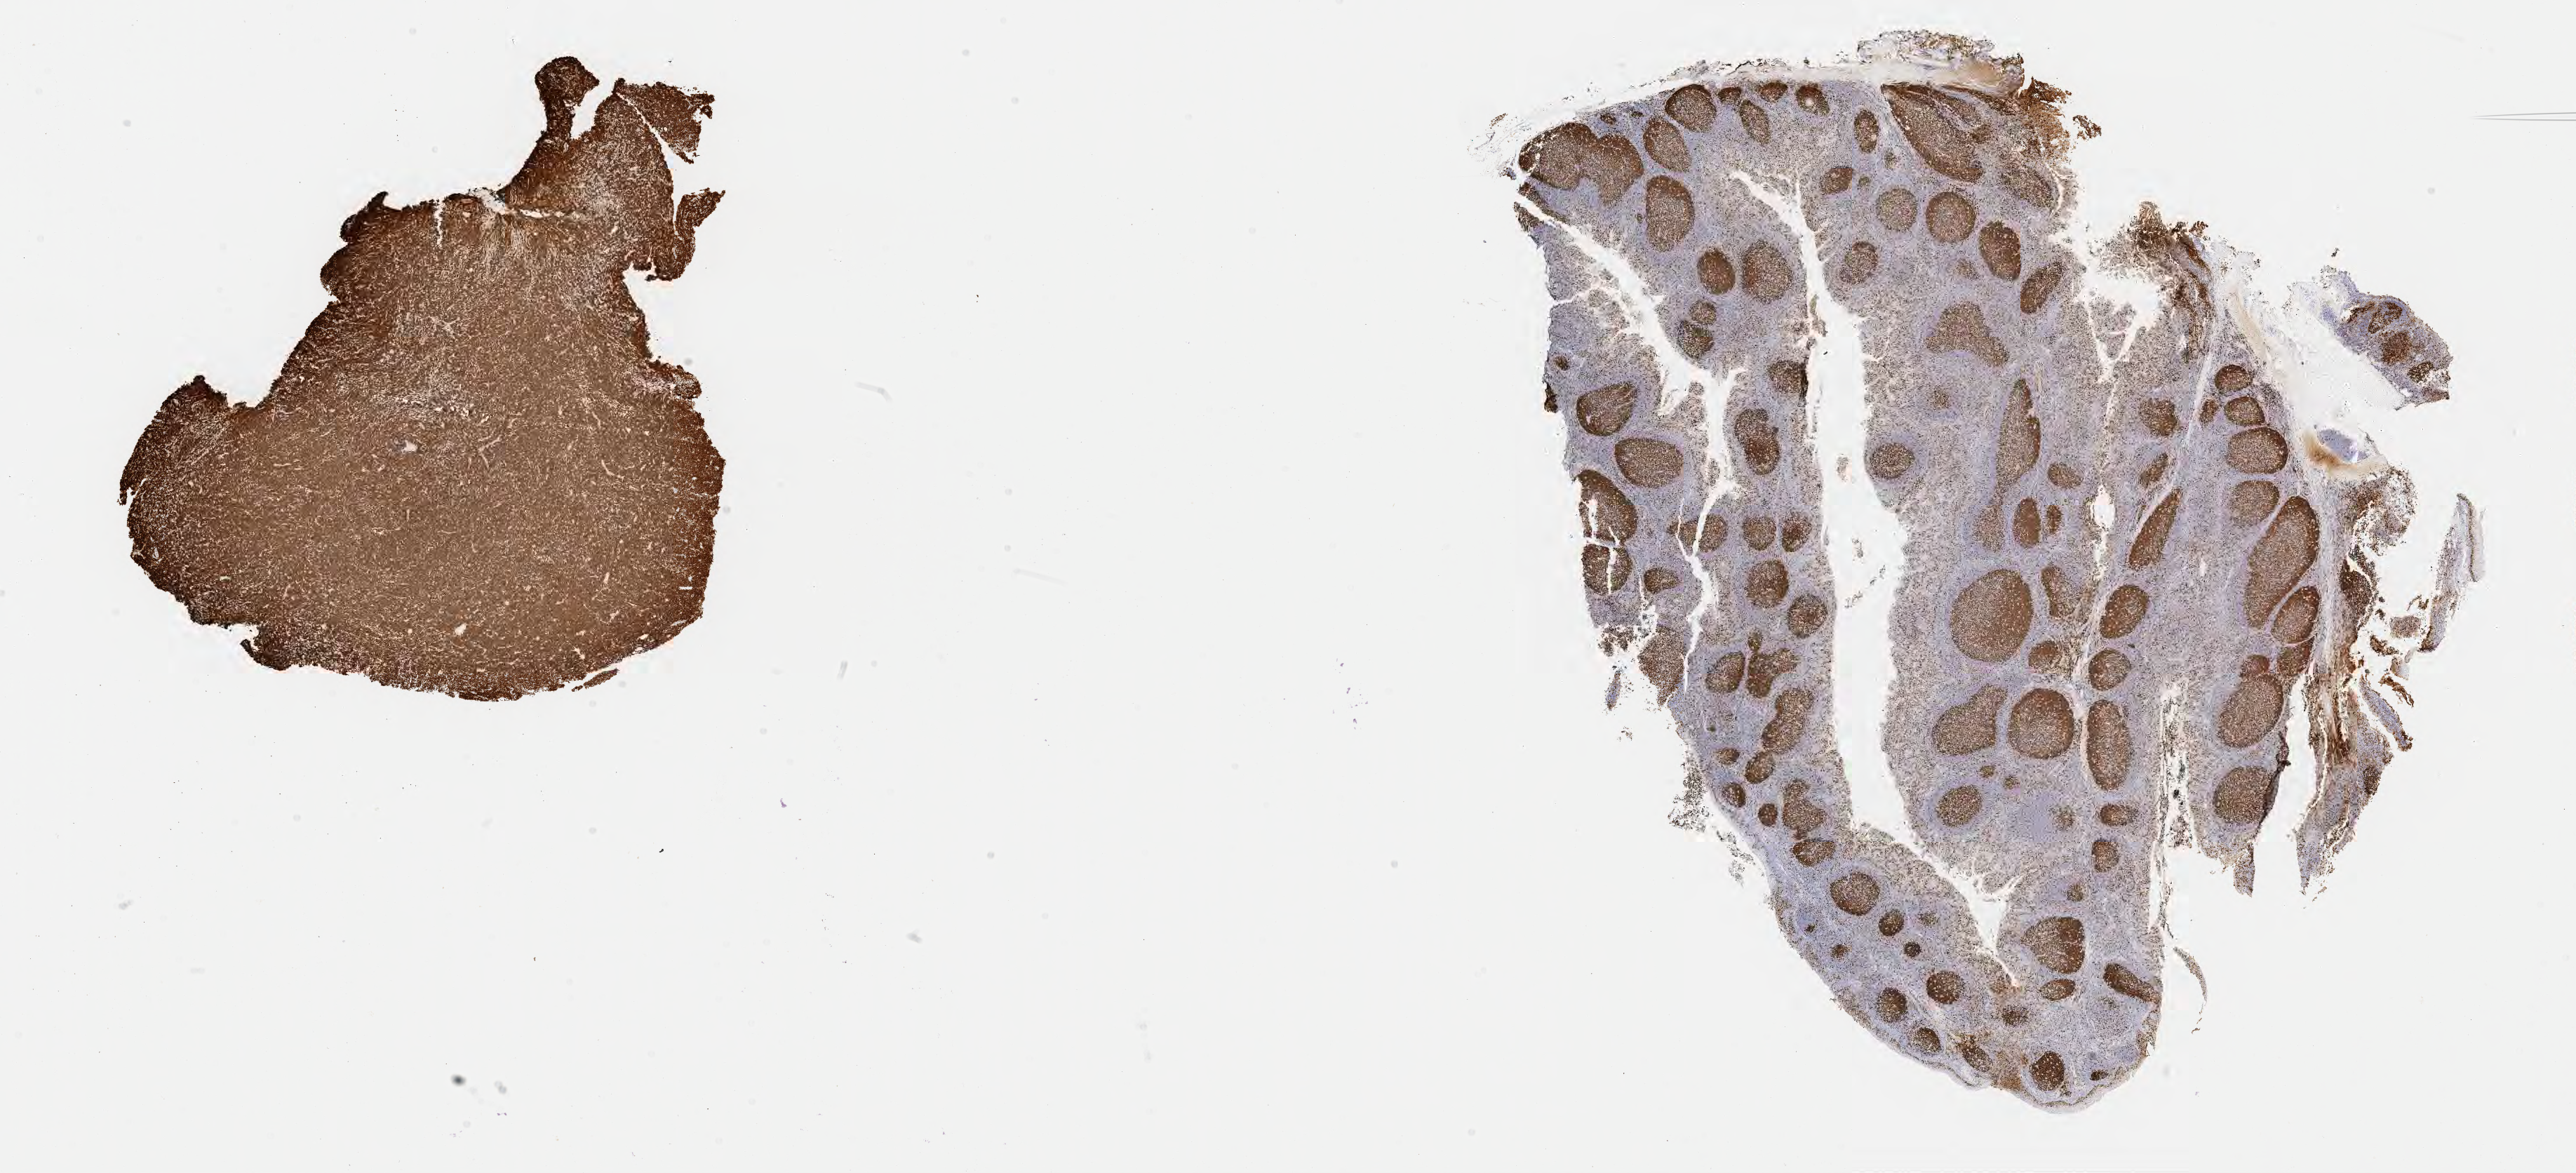
Immunohistochemistry (IHC) whole-slide image stained for Ki-67, shown as a low-resolution overview of the whole scanned area (about 29.7 x 13.5 mm). Specimen: tumor tissue. Anatomic site: mandible. Female, age 5 years at initial diagnosis.
- histologic diagnosis: Burkitt lymphoma, NOS